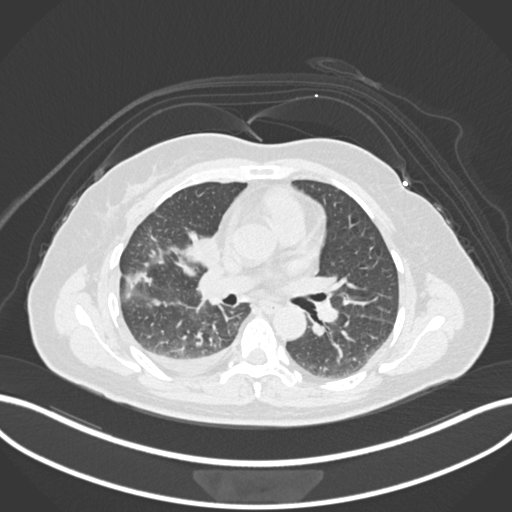
Chest CT, one axial slice; position 75 of 172 along the scan axis; lung window (W 1500 / L -600 HU); 1 mm slice thickness; 512 × 512 image matrix, field of view 400 × 400 mm. Patient: female, 52 years. Case-level facts recorded for this patient, not image findings: clinical TNM (as recorded): T3 N1 M1.
Outlined on this slice (bounding box drawn by a radiologist):
- lung tumour (recorded histology: adenocarcinoma): bounding box [x1, y1, x2, y2] px = [184, 232, 220, 268]